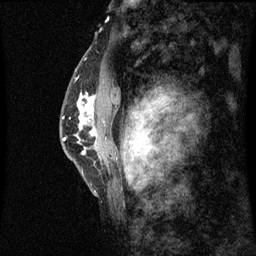
Breast MRI (dynamic contrast-enhanced), one sagittal slice; position 42 of 60 along the scan axis; dynamic contrast-enhanced series, image 2 of 3 at this slice position (ordered by acquisition); 1.5 T; TE 4.2 ms, TR 8.9 ms; 2 mm slice thickness; 256 × 256 image matrix. Patient: female, 50 years. From the clinical record (not read from this slice): setting: breast cancer imaged before/during neoadjuvant chemotherapy; receptor status: triple-negative.
Outlined on this slice (semi-automatic segmentation, software-assisted and operator-edited):
- analysis volume of interest (the breast-tissue region the enhancement analysis was run in; not a lesion): bounding box (x1, y1, x2, y2) in pixels: (68, 82, 99, 169)
- tumour enhancement mask (voxels above the 70 % enhancement threshold inside the analysis volume of interest): (81, 96, 95, 135)